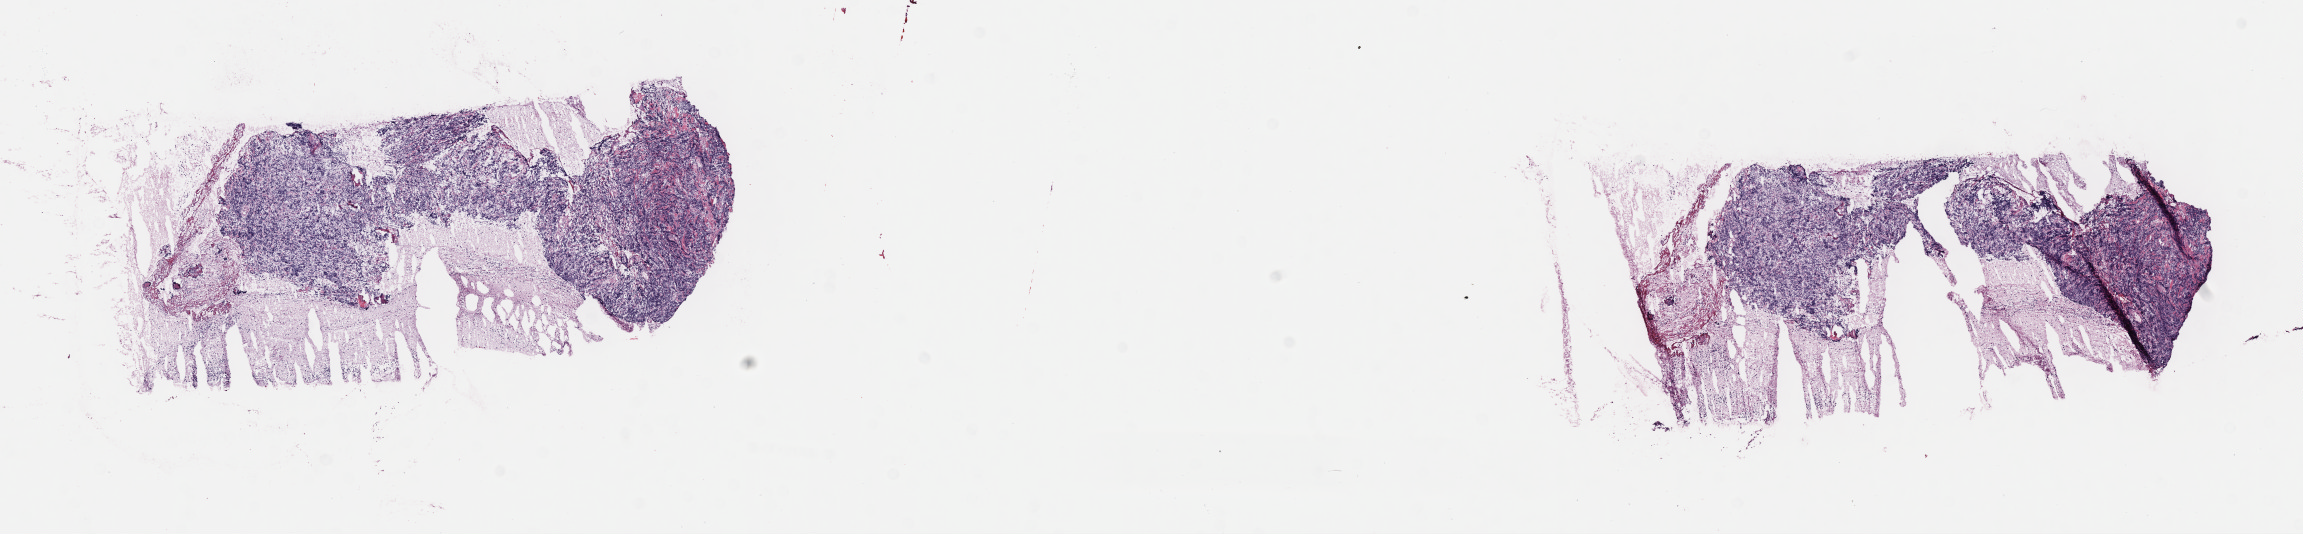
Whole-slide image, haematoxylin and eosin stain — low-resolution overview of the scanned area, about 18.6 x 4.3 mm; frozen section (tissue freezing medium); specimen: primary tumor; anatomic site: cranium. Female patient; age at initial diagnosis 5 years. Composition of this section per pathologist review: tumor cells 90%, tumor nuclei 90%, stromal cells 7%, necrosis 3%, normal cells 0%. Inflammatory infiltration, as recorded: lymphocyte infiltration 2%, monocyte infiltration 3%, neutrophil infiltration 0%.
Diagnosis: Burkitt lymphoma, NOS. Ann Arbor stage (patient): Stage IV. Section: top of the tissue portion.